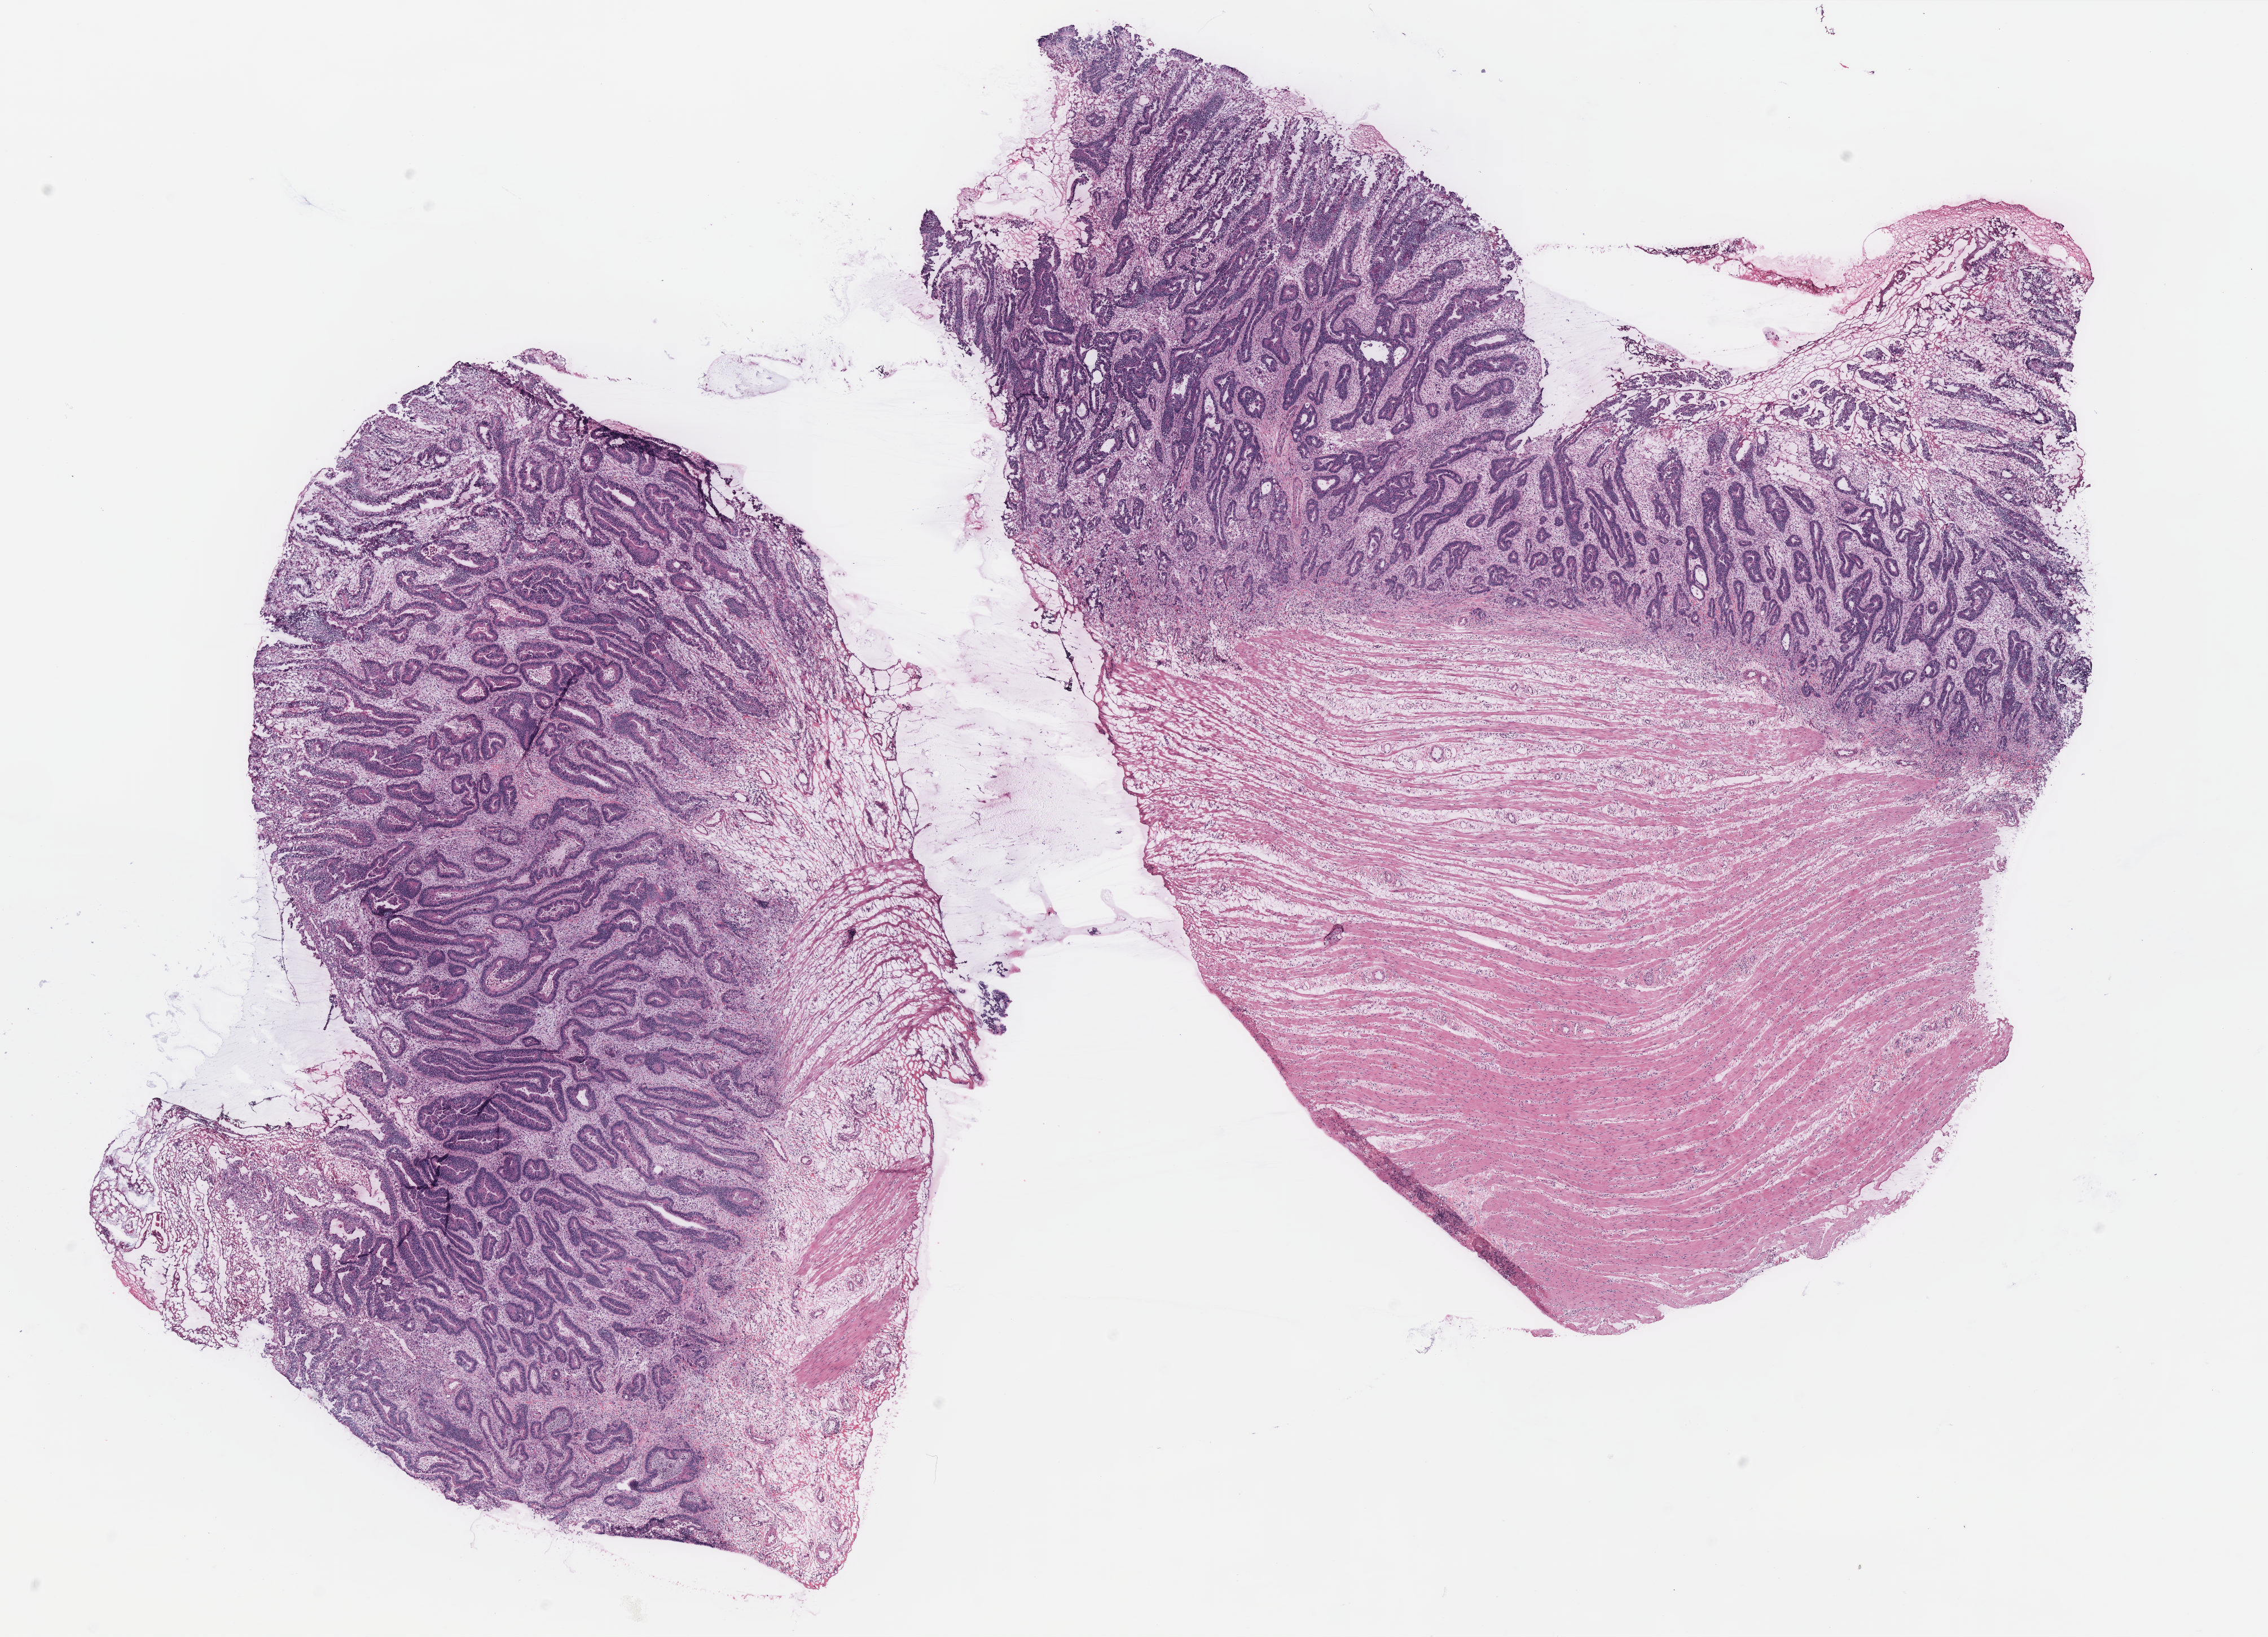
Digitized Hematoxylin and eosin (H&E) stained tissue section (whole slide) — low-resolution overview of the scanned area, about 16.1 x 11.6 mm (acquisition: 40x scan). Colon, tissue type not recorded.
Patient diagnosis (cohort enrolment): colon cancer (colon).